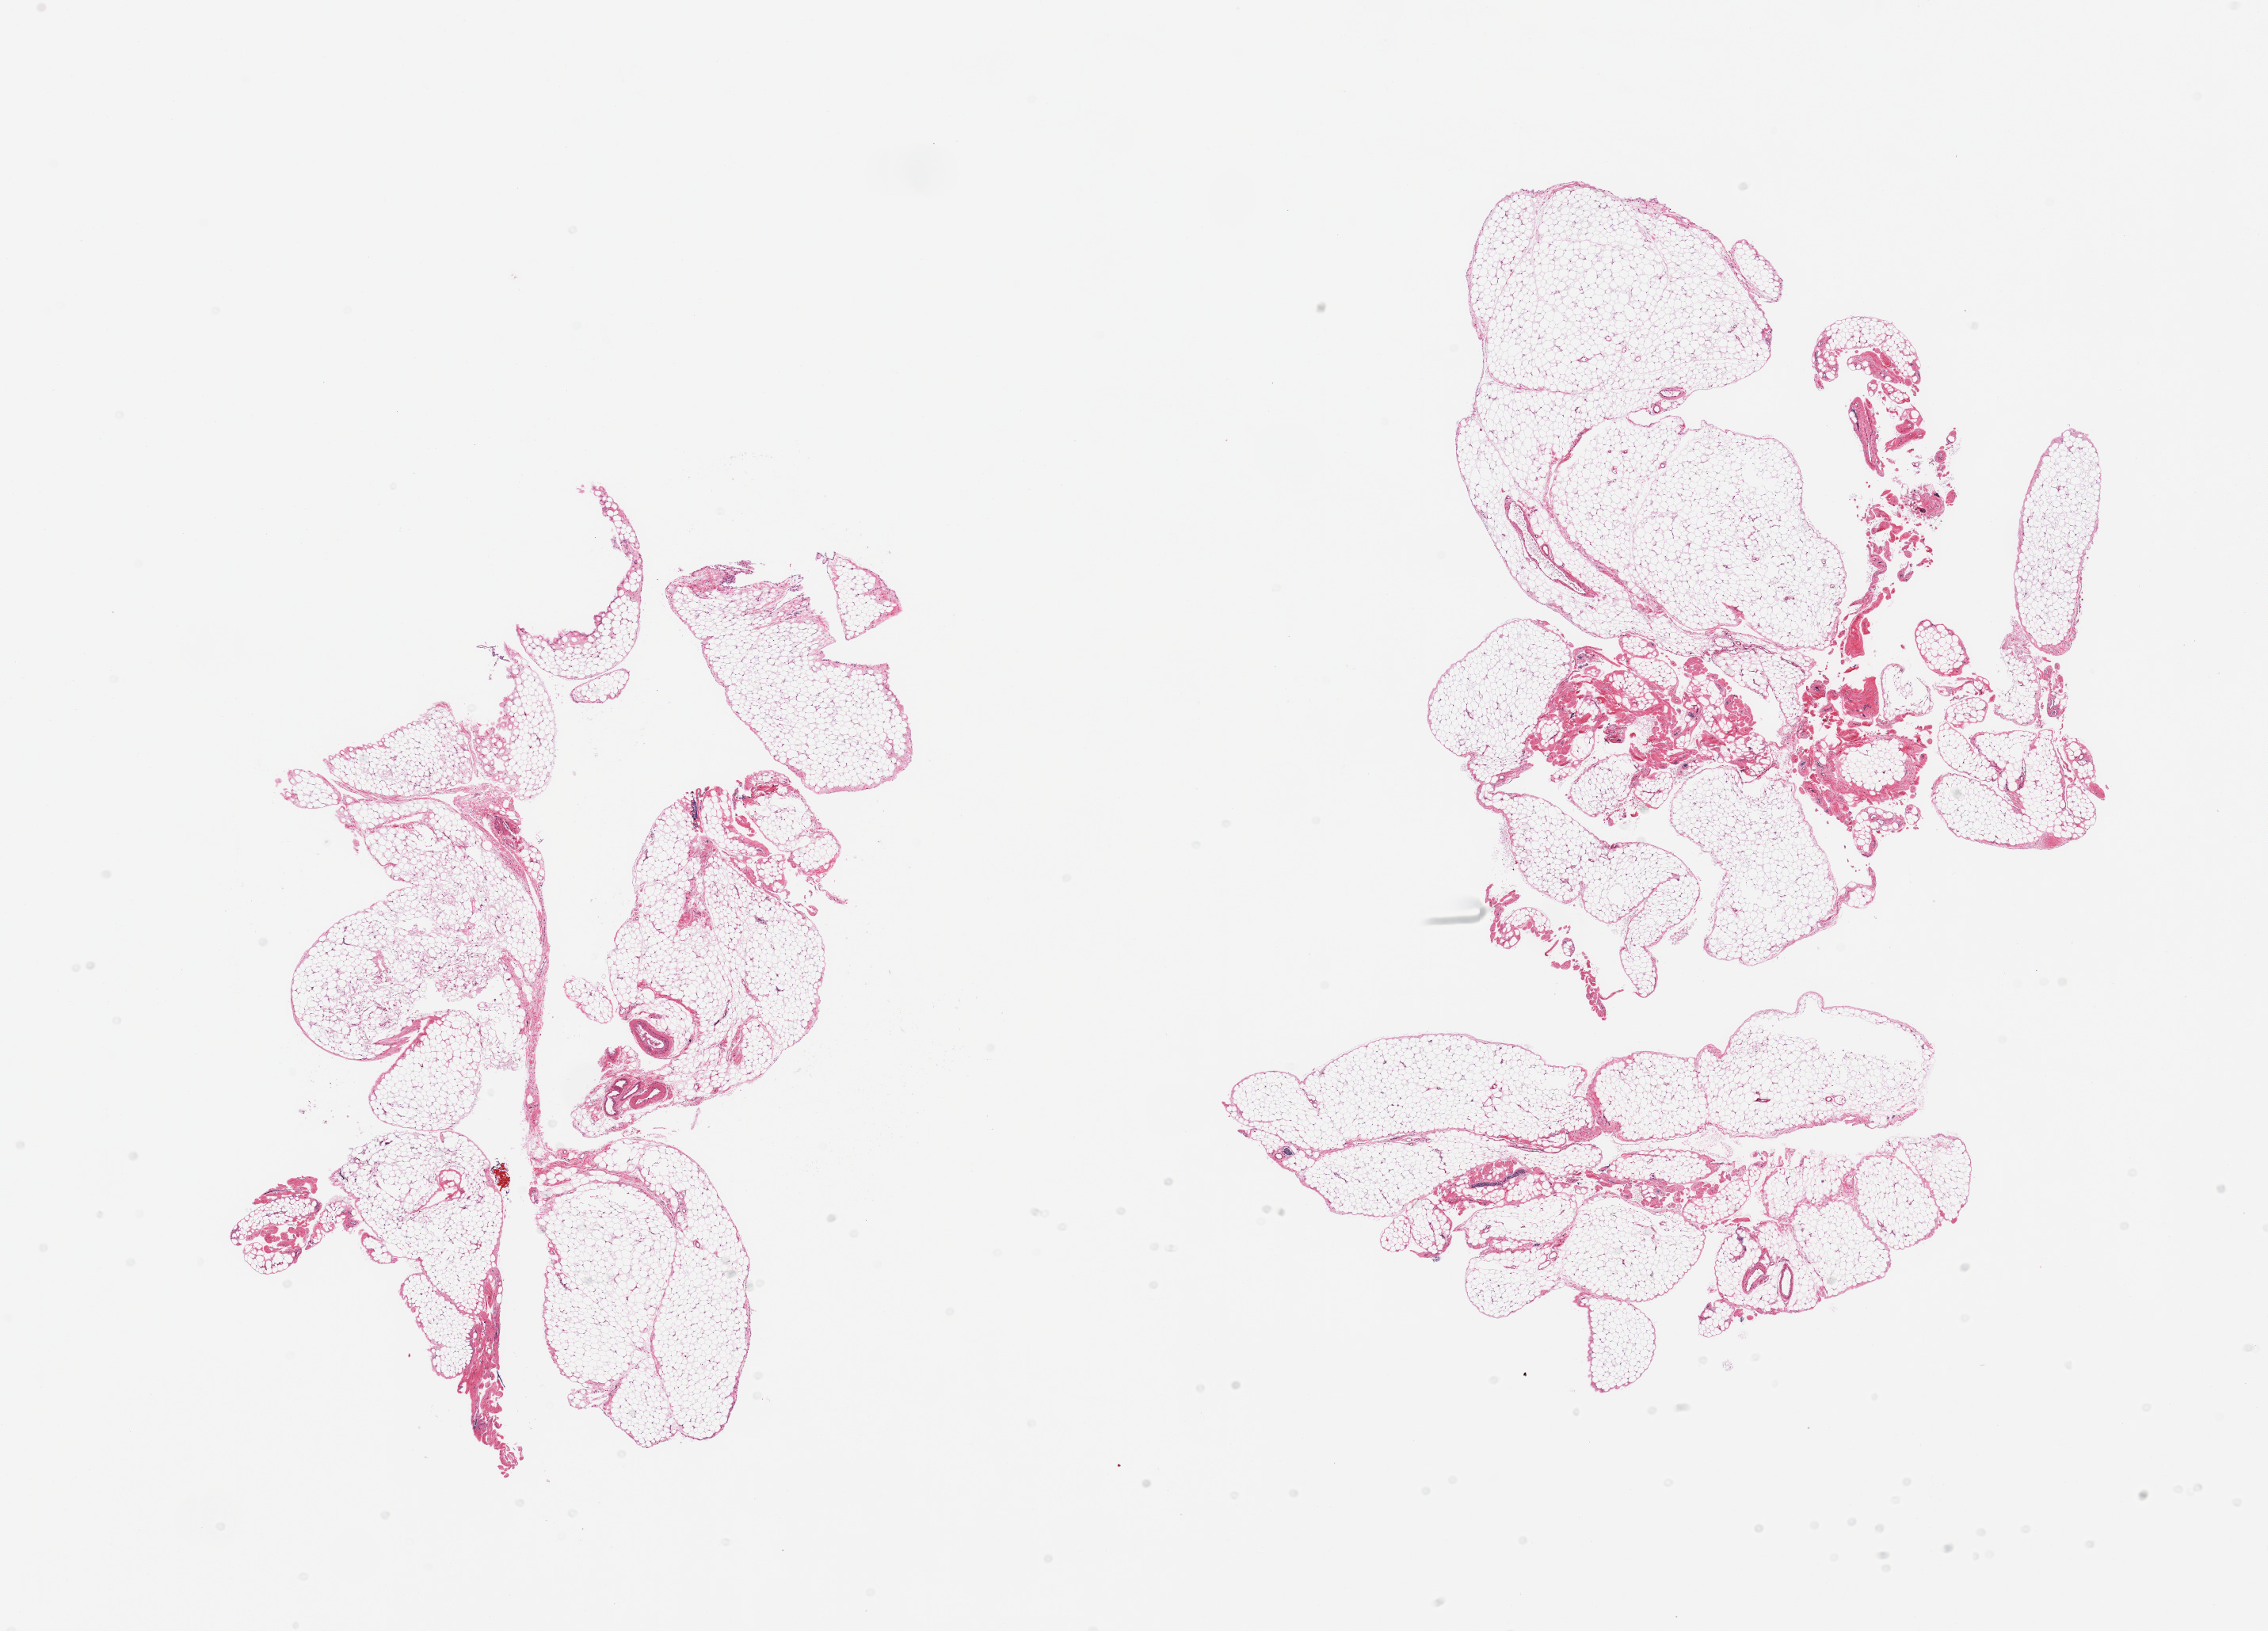
Whole-slide image, haematoxylin and eosin stain — whole scanned area (about 22.6 x 16.3 mm, acquisition: 20x scan) shown as a low-resolution overview. PAXgene-fixed, paraffin-embedded tissue. Section of omentum (target tissue). Tissue donor sample. Male donor.
Reviewer comment on this tissue sample: 2 pieces, ~10-15% fascia/vascular elements.